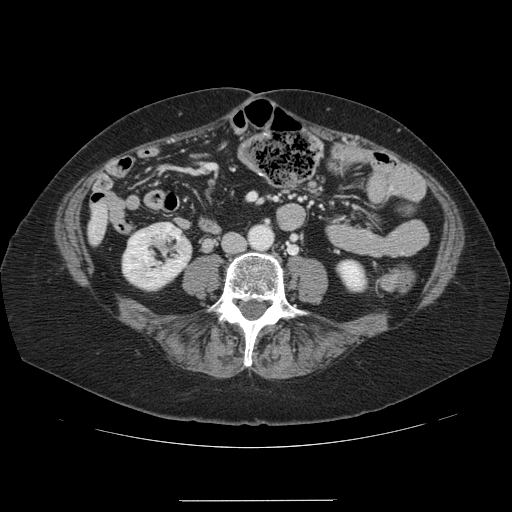
Contrast-enhanced abdominal CT, one axial slice. Slice 11 of 141 in the series (ordered by position). Intravenous contrast given. Soft-tissue window (W 400 / L 40 HU). 2.5 mm slice thickness. 512 × 512 image matrix, field of view 393 × 393 mm. Female patient, age 74 years. From the clinical record (not read from this slice): diagnosis: colorectal cancer liver metastases, imaged before liver resection; multiple liver metastases: yes; largest metastasis: 7 cm; disease in both lobes: yes.
Structures marked on this image (outlined manually by an expert reader):
- liver: bounding box <90,207,108,242> (left, top, right, bottom; pixels)
- planned liver remnant (the part of the liver to remain after resection): <99,219,108,241>